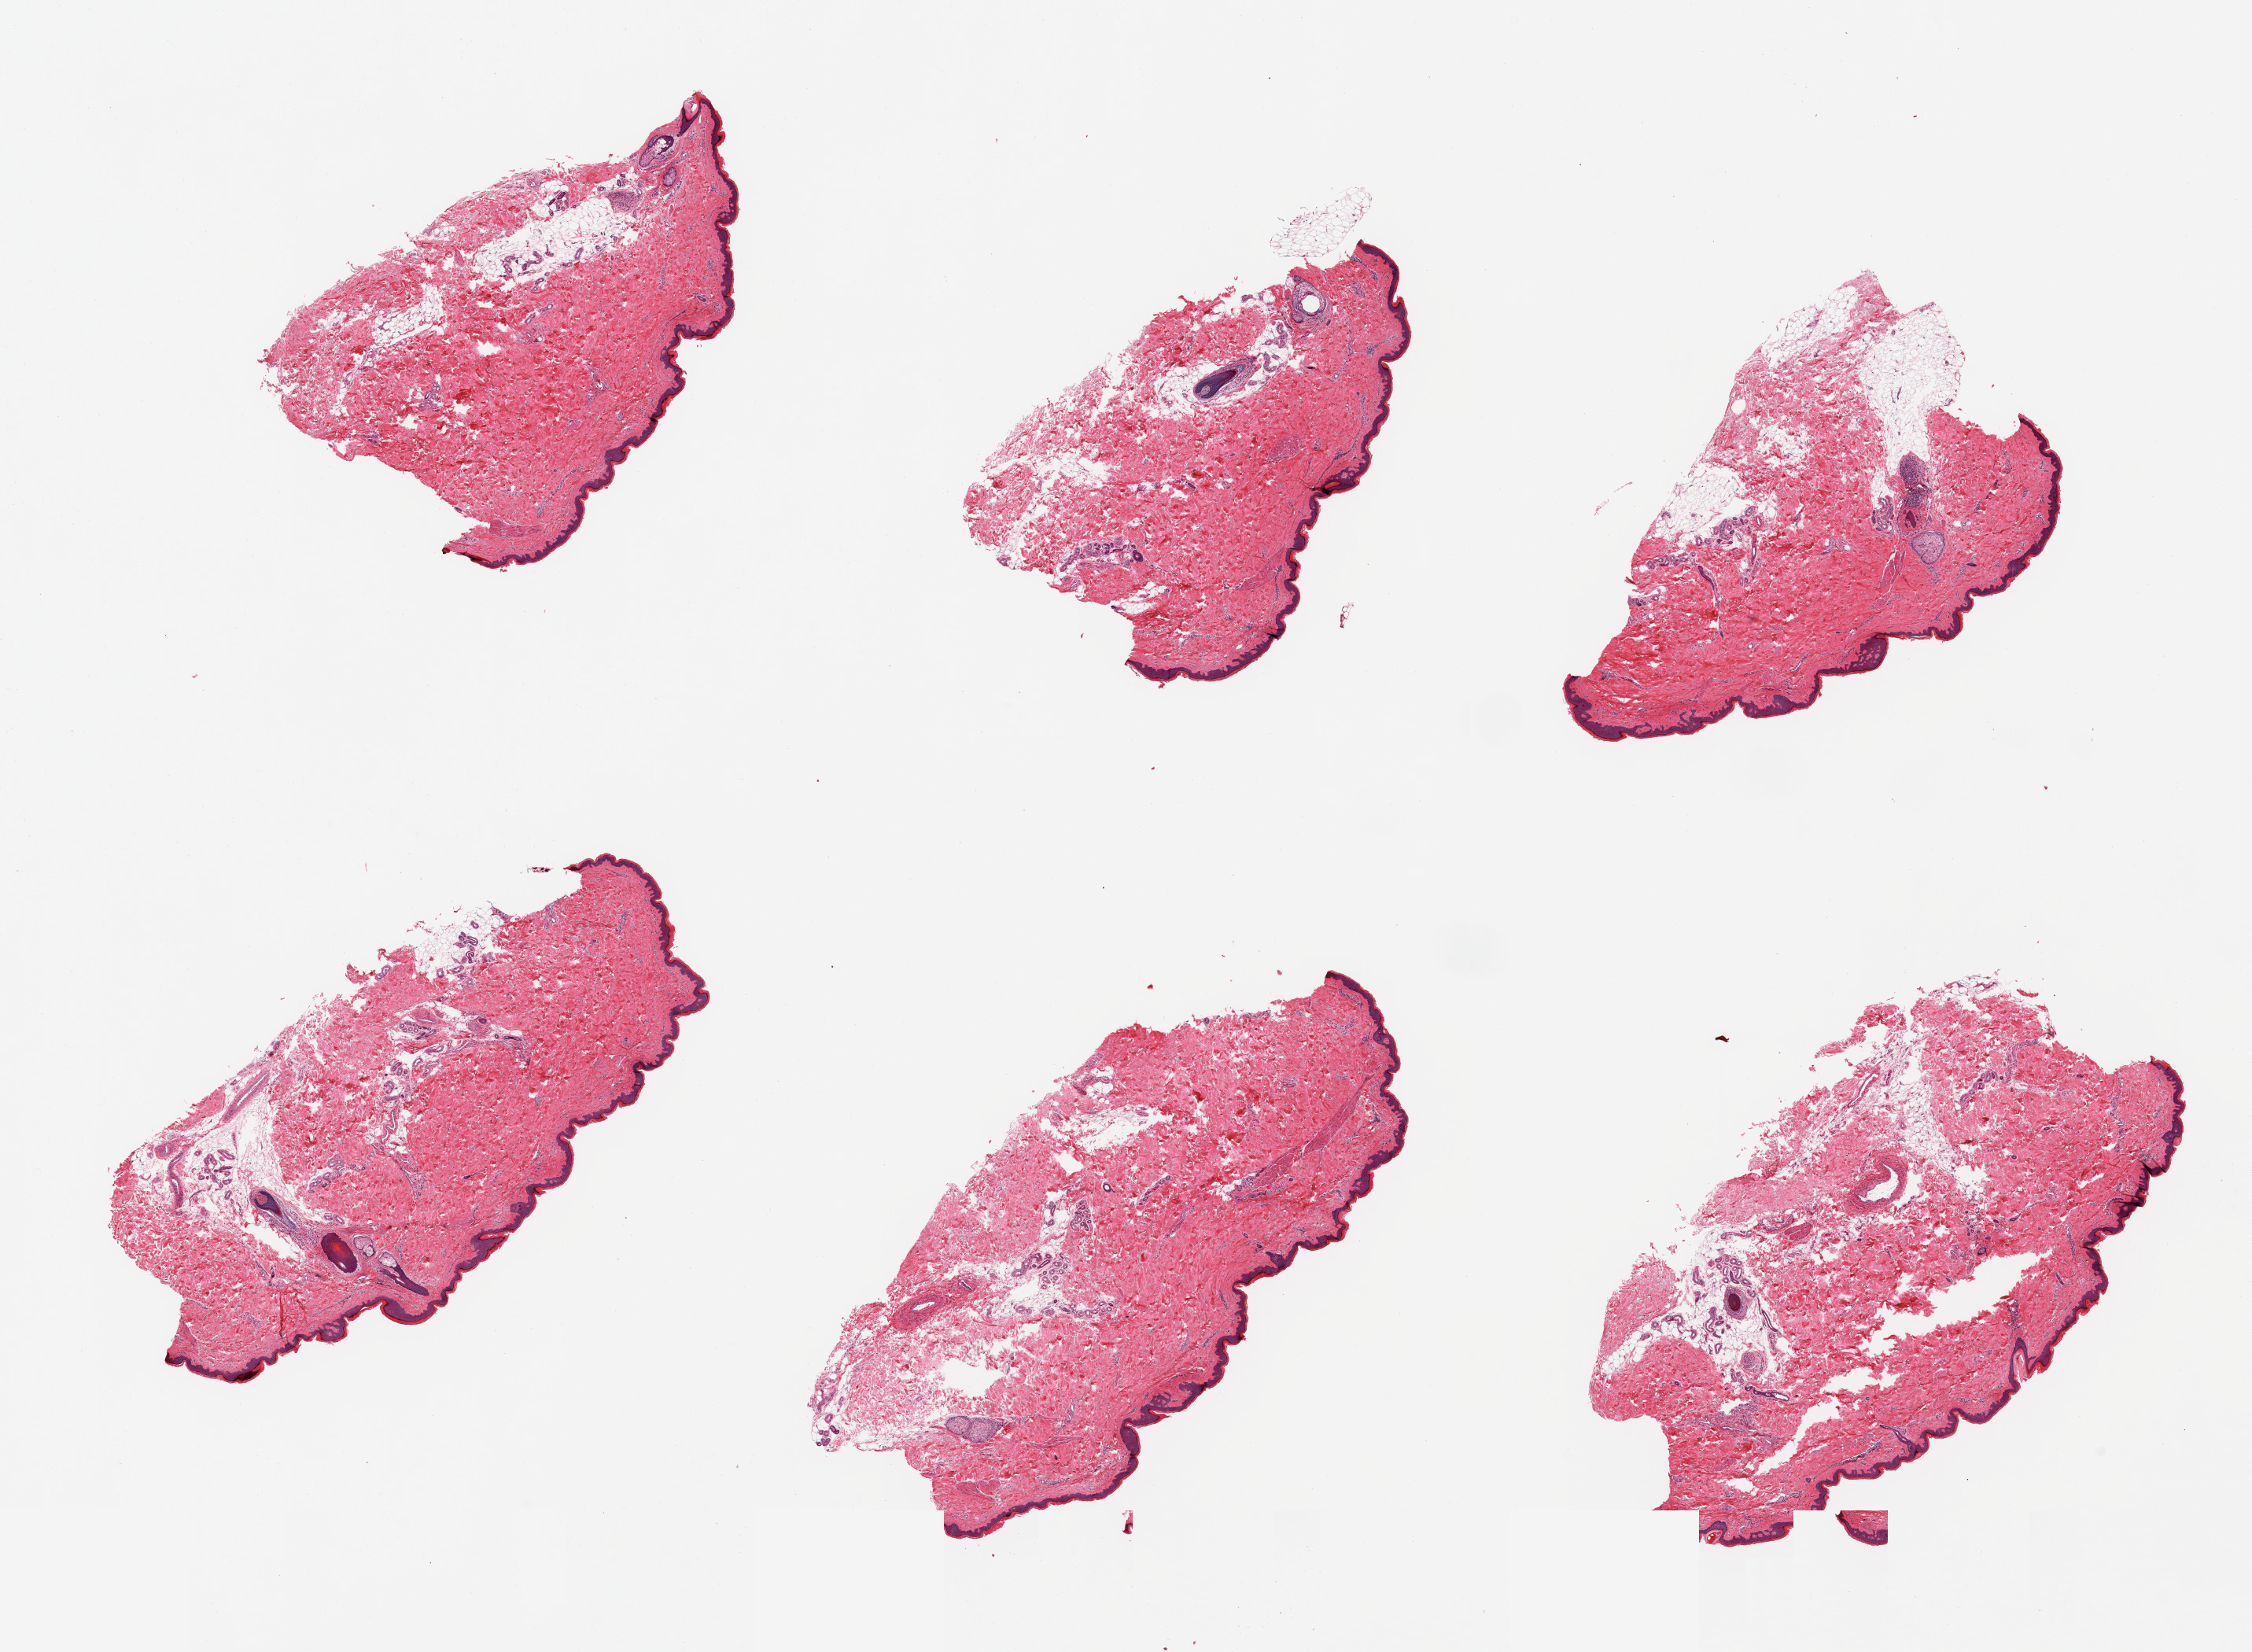
Digitized H&E-stained section, brightfield, low-resolution overview of the scanned area, about 22.6 x 16.6 mm, PAXgene-fixed paraffin-embedded (PFPE) section, target tissue: skin of lower leg, donor tissue sample. Donor: male.
• review note (as recorded): 6 pieces, trace dermal fat, squamous epithelium is ~50 microns